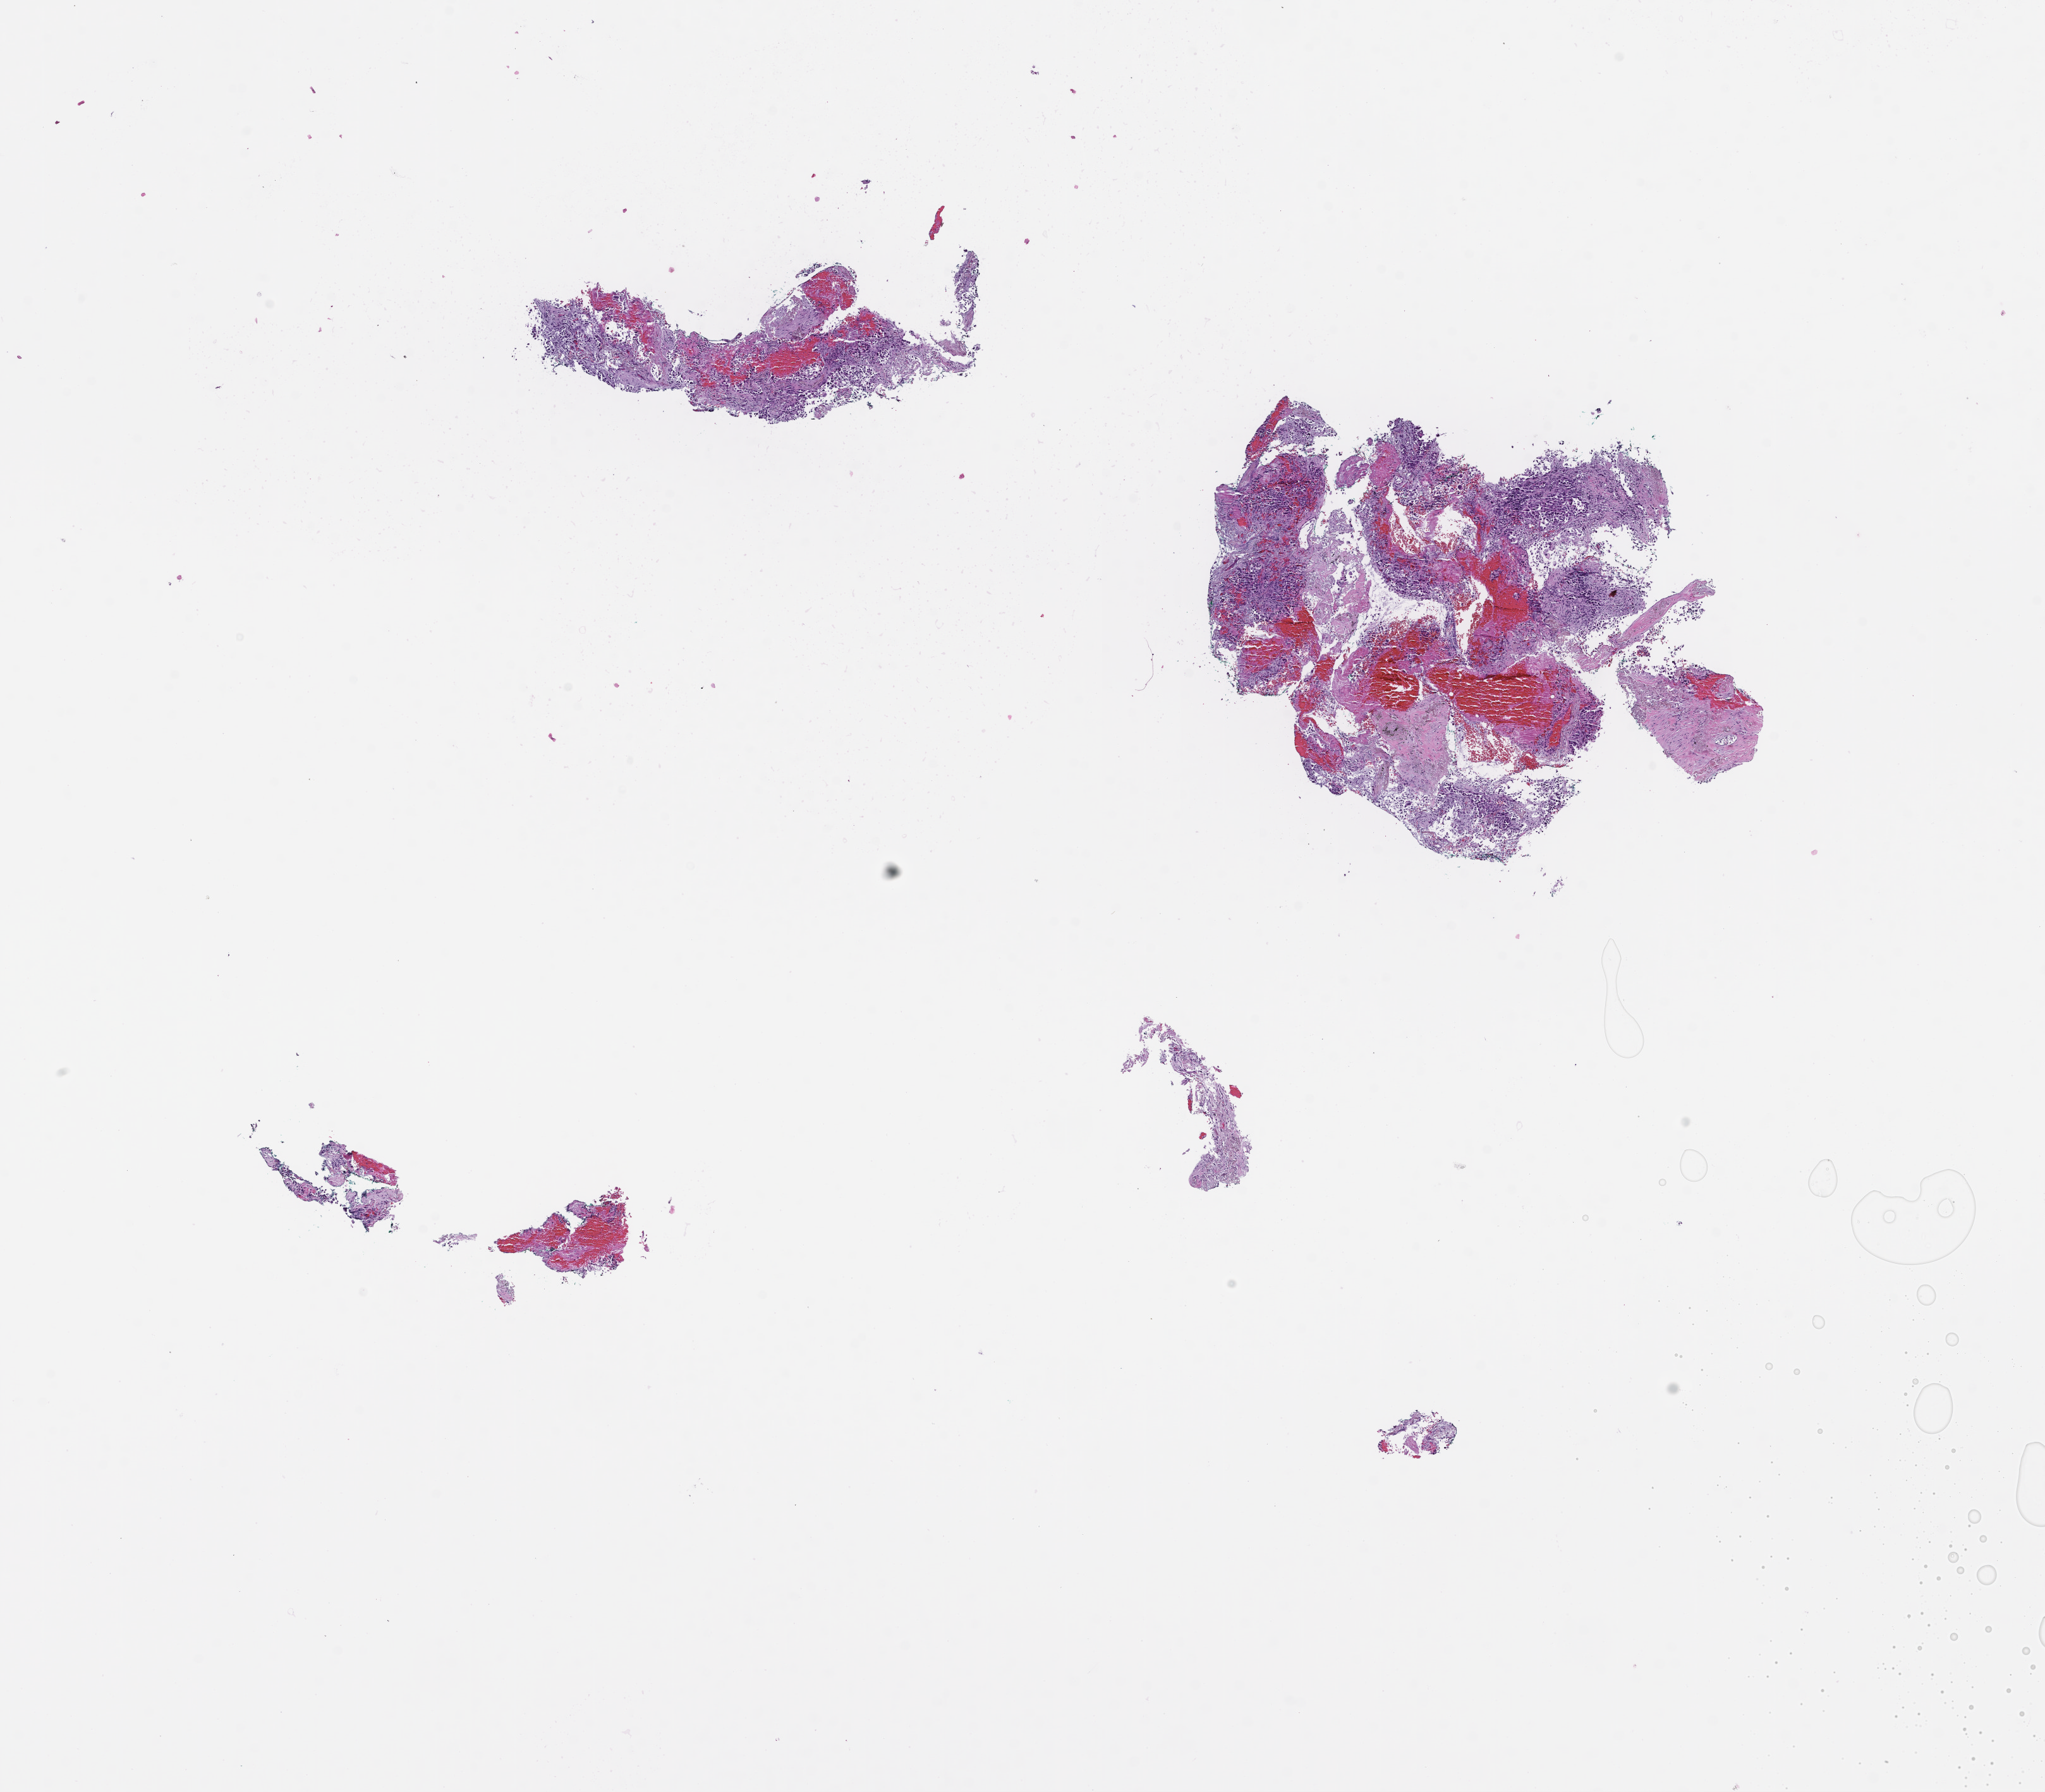
Hematoxylin and eosin (H&E) whole-slide image, shown as a low-resolution overview of the whole scanned area (about 13.1 x 11.5 mm), formalin-fixed paraffin-embedded section. Patient: female.
This section: metastatic tumor tissue. Patient diagnosis (primary): Non-Small Cell Lung Carcinoma.